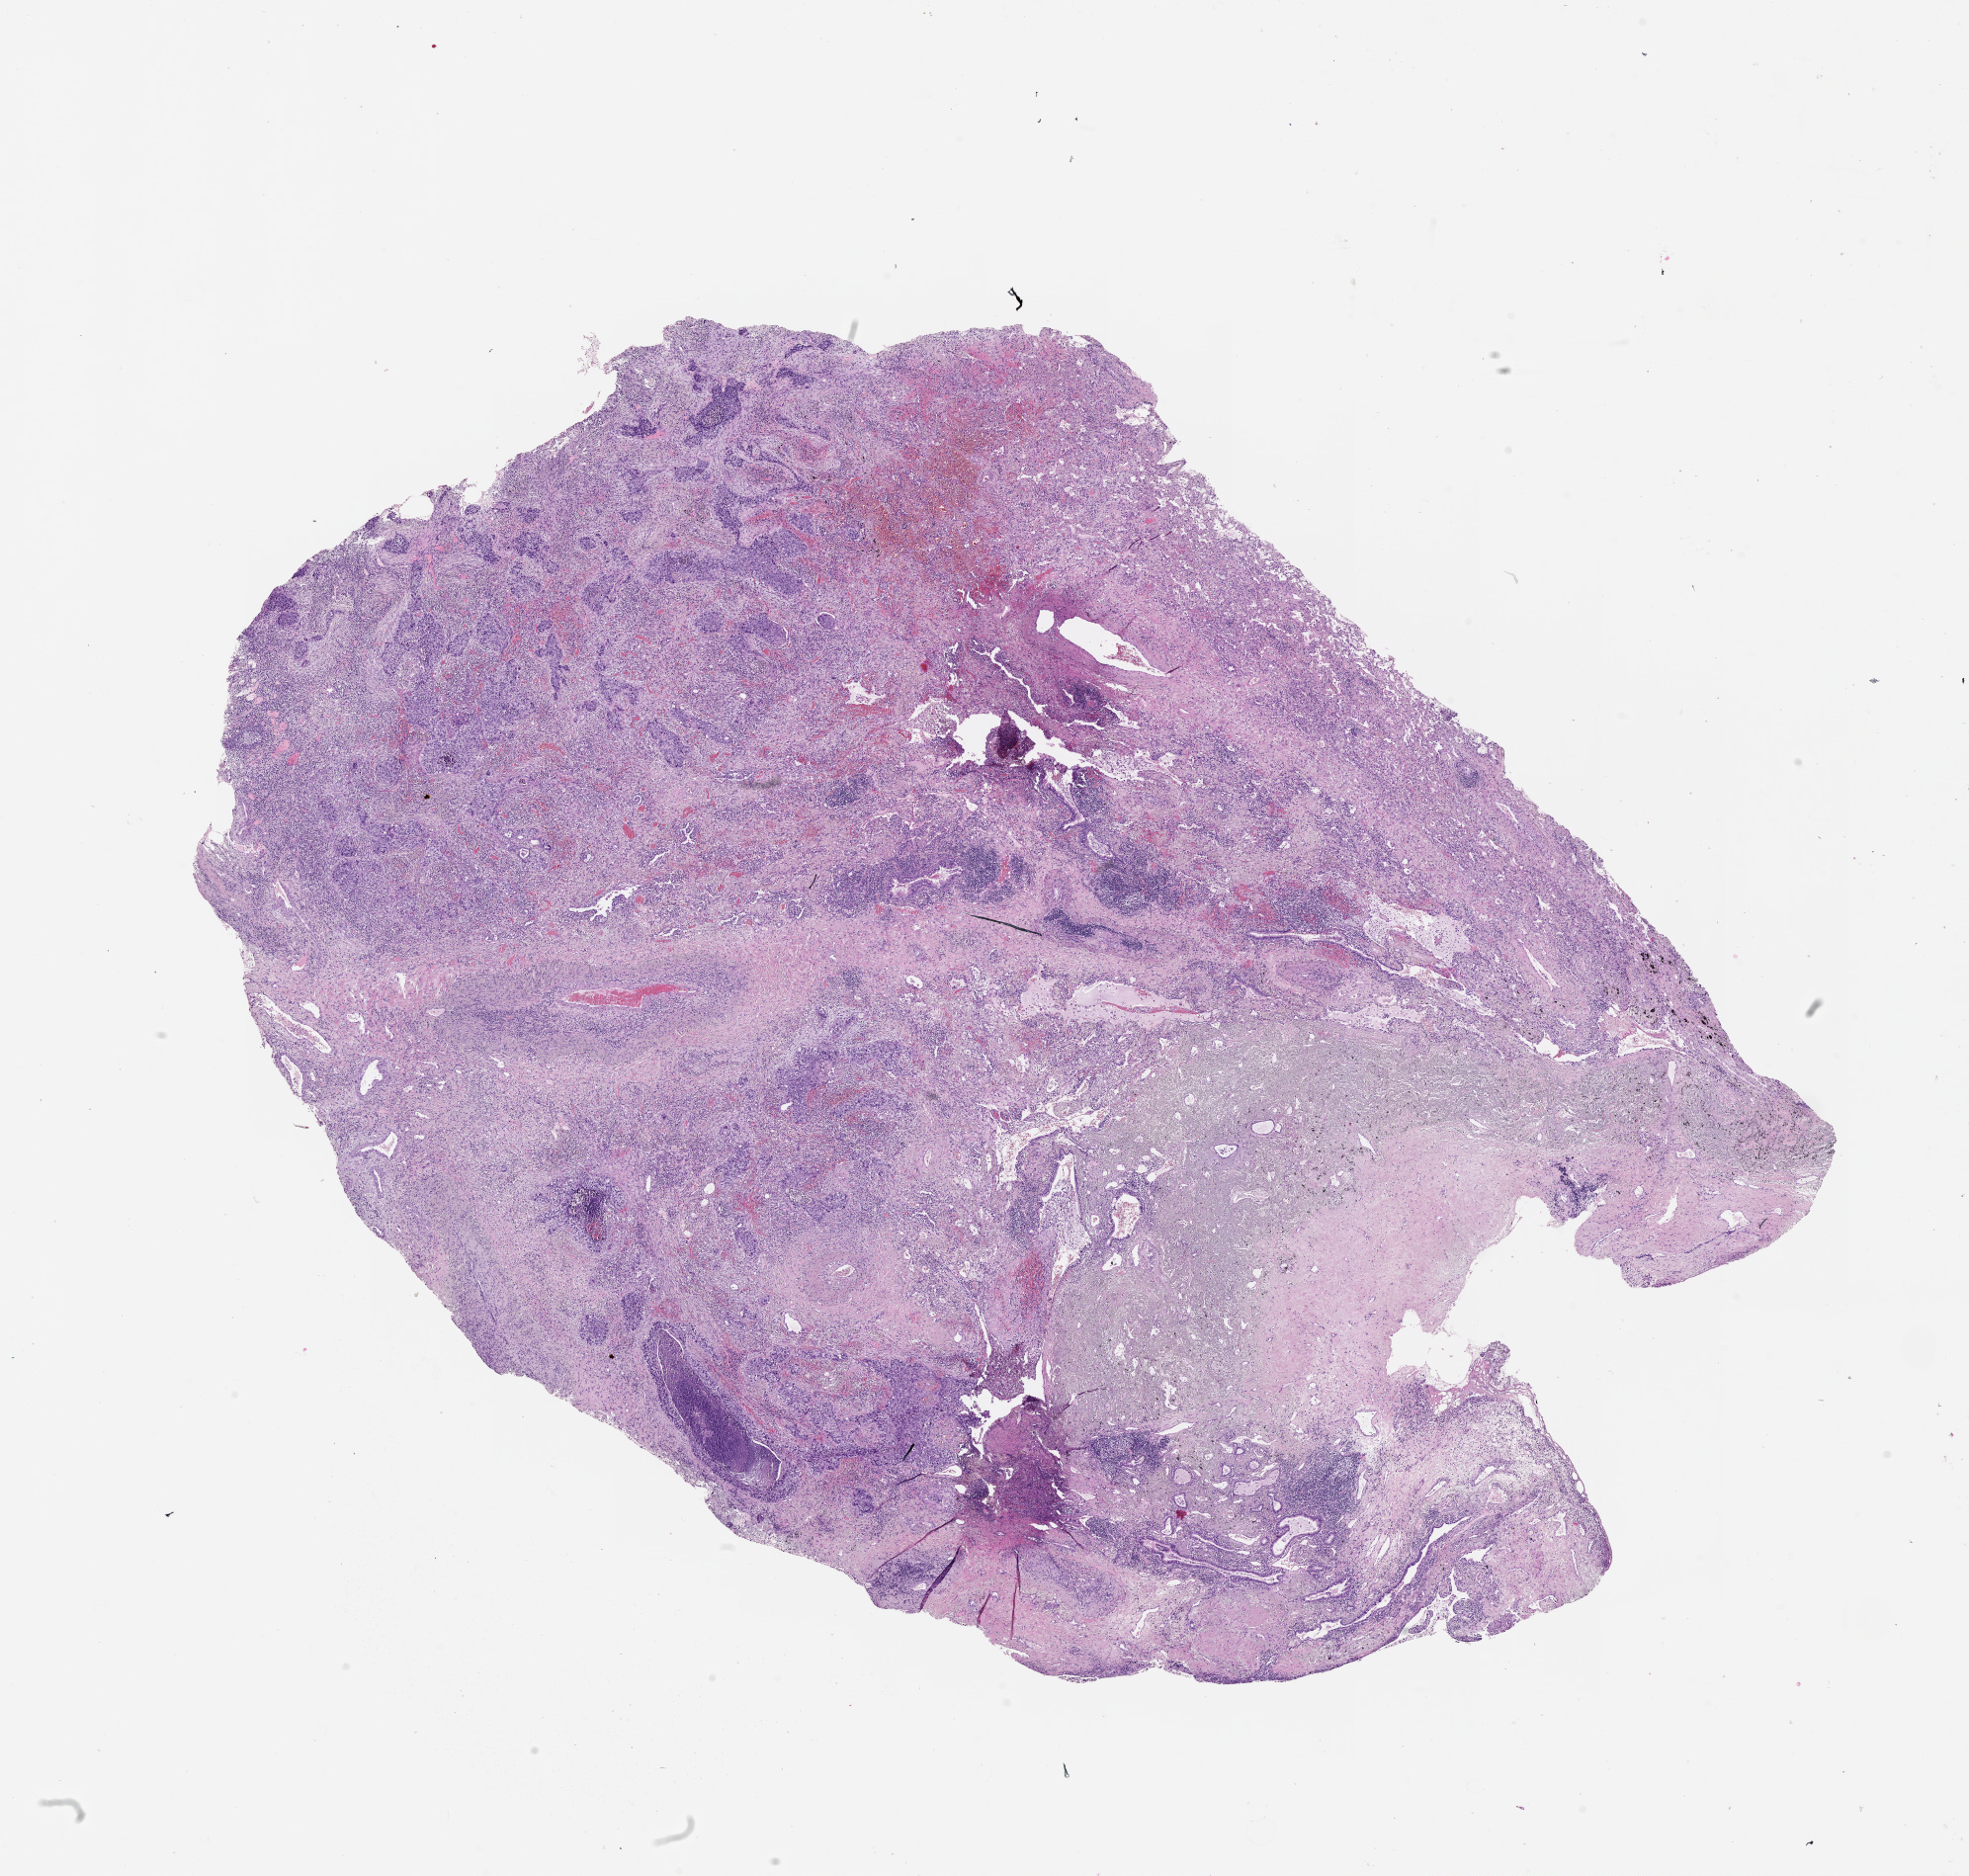
Whole-slide histology image, H&E, whole scanned area (about 16.0 x 15.3 mm, acquisition: 20x scan) shown as a low-resolution overview, tumour tissue sample, lung. Male, 77 y/o.
Patient diagnosis (cohort enrolment): squamous cell carcinoma (lung).